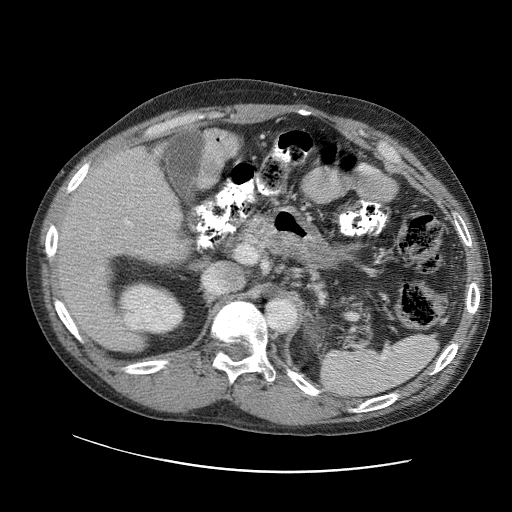
Contrast-enhanced abdominal CT (liver protocol), one axial slice. Slice 62 of 109 in the series (ordered by position). Reconstruction kernel STANDARD. 120 kVp. Soft-tissue window (W 400 / L 40 HU). 2.5 mm slice thickness. 512 × 512 image matrix, field of view 400 × 400 mm. From the clinical record (not read from this slice): diagnosis: hepatocellular carcinoma (patient treated with transarterial chemoembolisation; whether this scan precedes or follows treatment is not stated here); TNM stage (as recorded): Stage-IIIC; Child-Pugh class: B; tumour differentiation: well differentiated; tumour nodularity: uninodular.
Structures marked on this image (semi-automatically segmented with operator editing):
- liver parenchyma outside the tumour (the mass and vessels are separate outlines, so this box may not span the whole liver): bounding box [x1, y1, x2, y2] px = [54, 146, 188, 330]
- liver vessels: [83, 184, 163, 290]